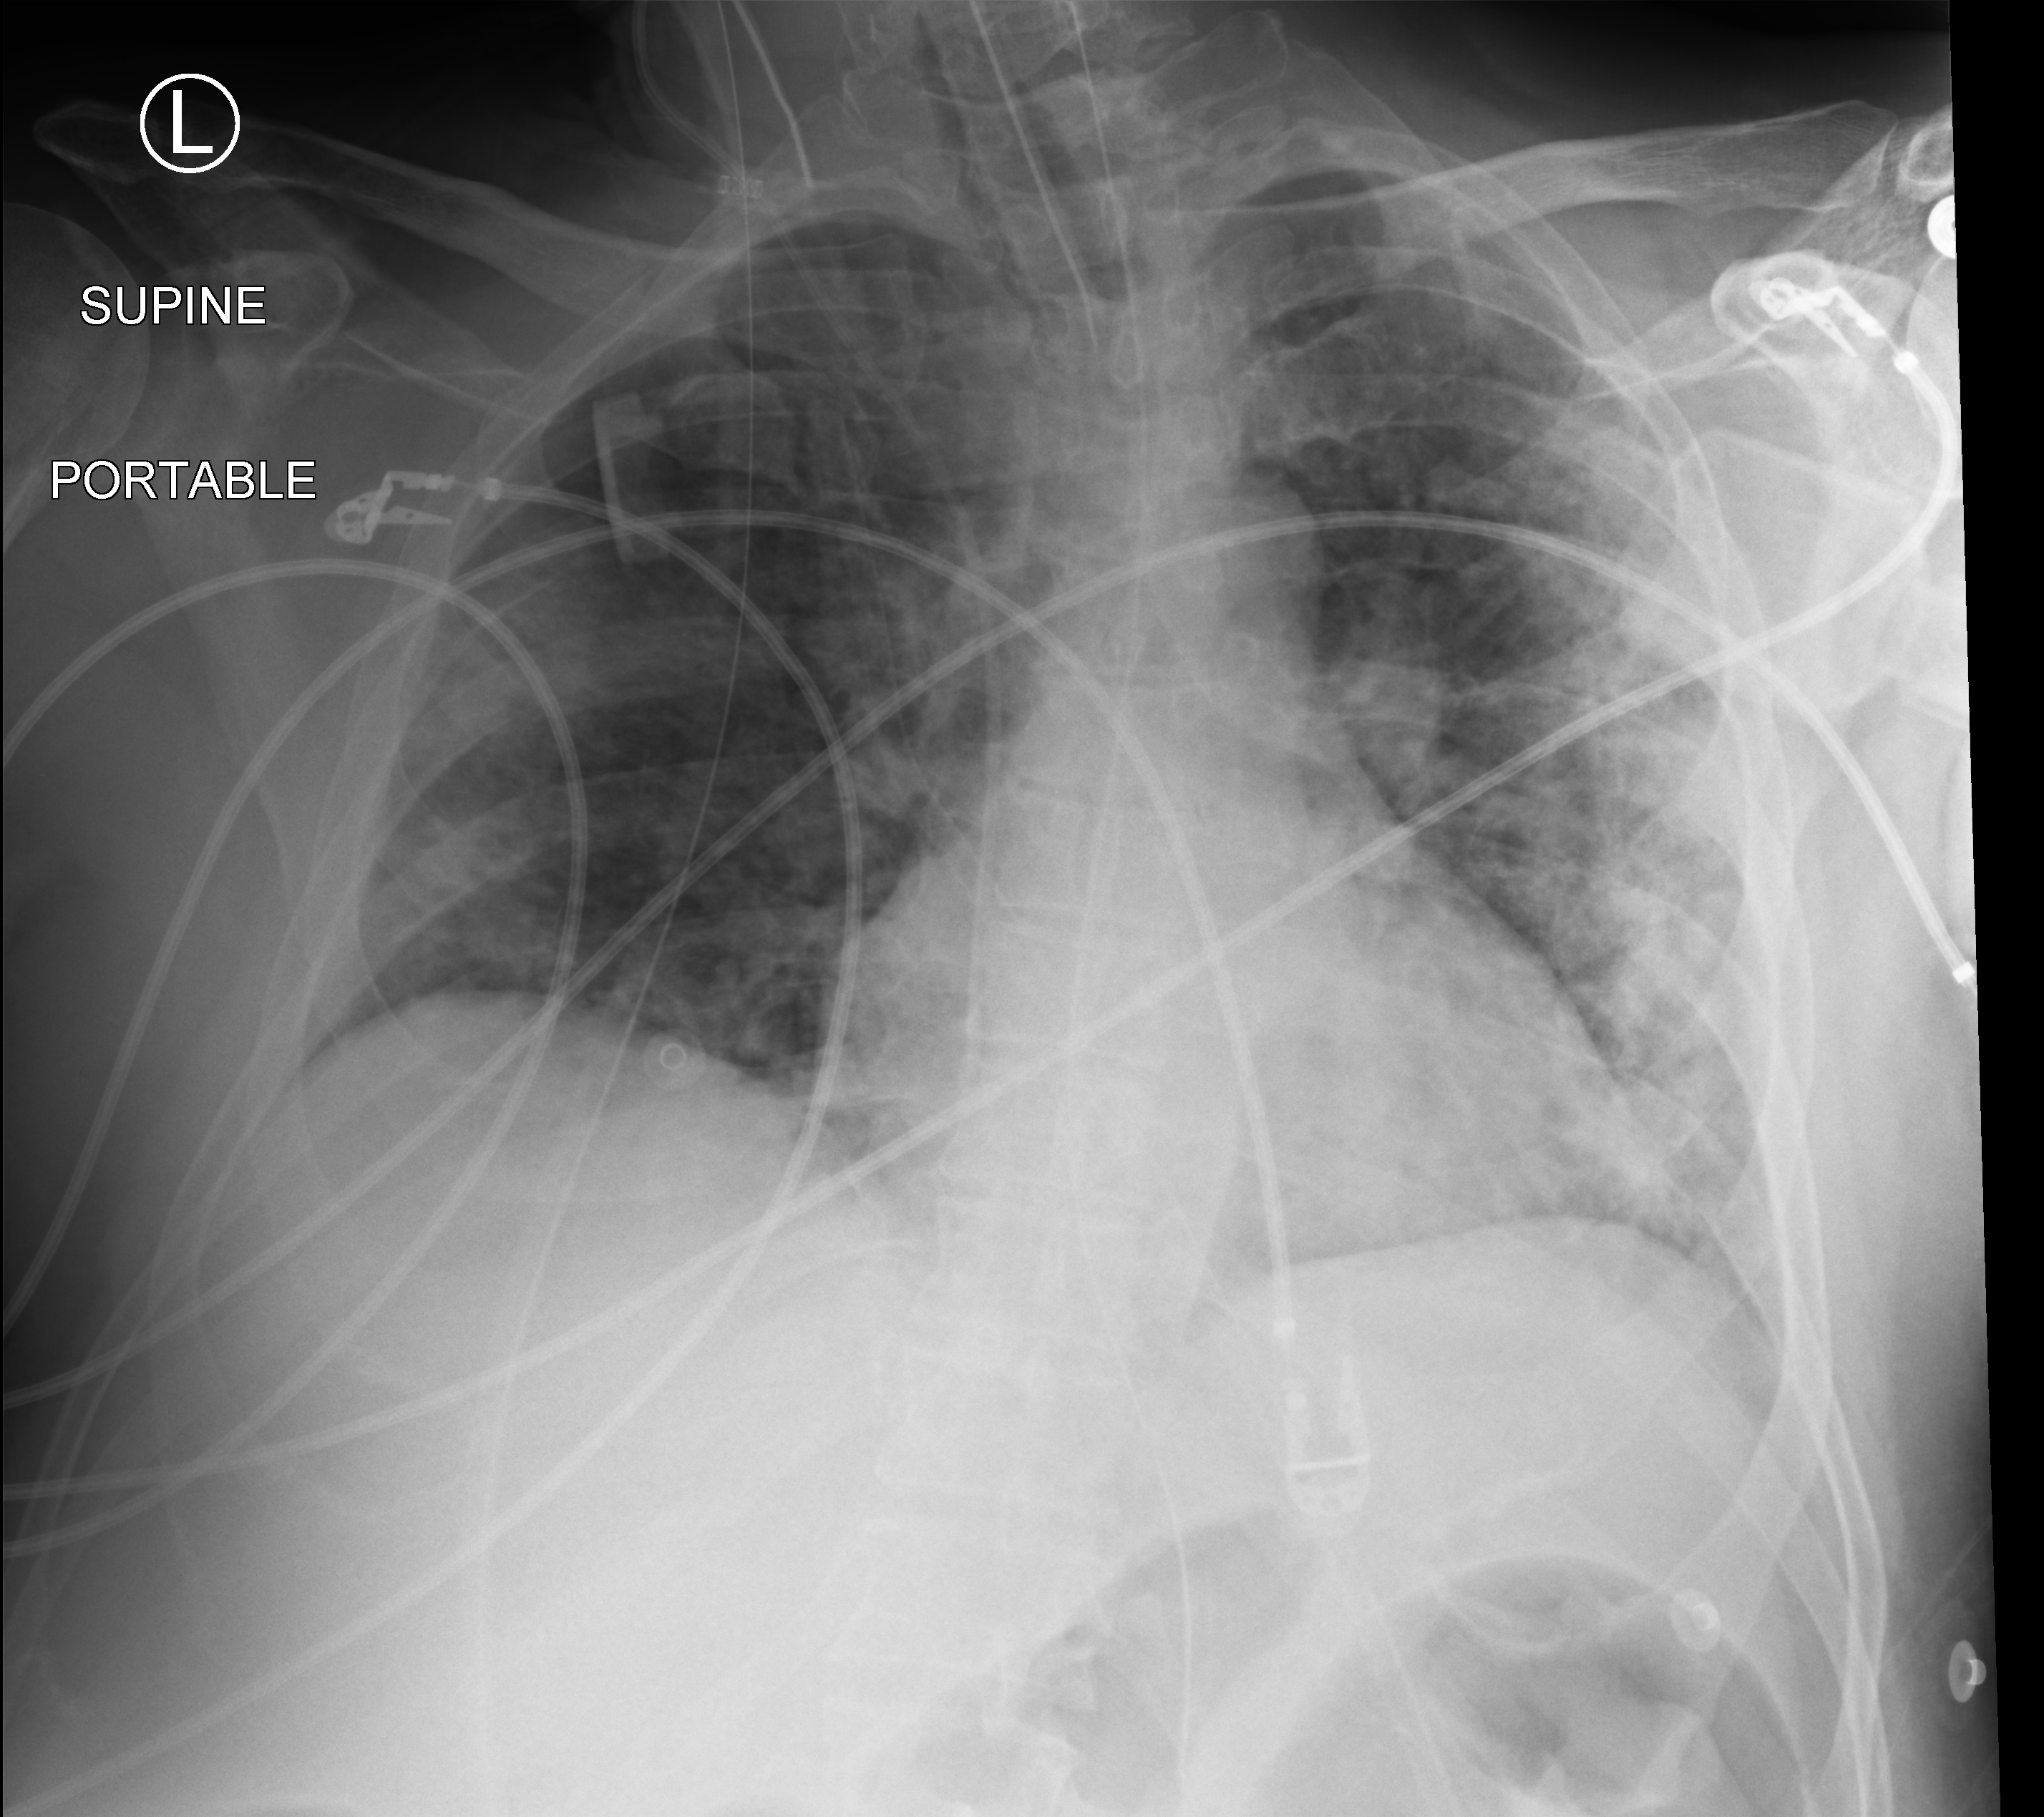
Bedside chest radiograph (computed radiography); anteroposterior (AP) projection. Male patient hospitalised with COVID-19, age 18–59 years.
From the hospital-stay record, not from the radiograph (when in the stay this image was taken is not recorded): mechanically ventilated during this hospital stay: yes.